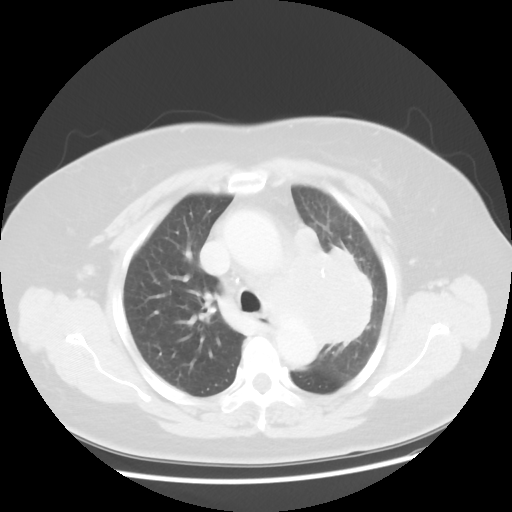
Chest CT, one axial slice. Position 33 of 49 along the scan axis. Reconstruction kernel STANDARD. Lung window (W 1500 / L -600 HU). 512 × 512 image matrix. Female patient, age 58 years. From the clinical record (not read from this slice): clinical TNM (as recorded): T4 N3 M0.
Structures marked on this image (bounding box drawn by a radiologist):
- lung tumour (recorded histology: small cell carcinoma): bounding box (x1, y1, x2, y2) in pixels: (275, 214, 391, 358)